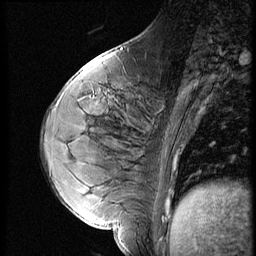
Breast MRI (dynamic contrast-enhanced), one sagittal slice. Slice 21 of 56 in the series (ordered by position). 3 images stored at this slice position (order not interpretable as contrast timing). 1.5 T. TE 4.2 ms, TR 9 ms. 2.5 mm slice thickness. 256 × 256 image matrix, field of view 180 × 180 mm. Patient: female, 35 years. From the clinical record (not read from this slice): setting: breast cancer imaged before/during neoadjuvant chemotherapy; receptor status: HR-positive, HER2-negative.
Outlined on this slice (semi-automatically segmented with operator editing):
- analysis volume of interest (the breast-tissue region the enhancement analysis was run in; not a lesion): bounding box [x1, y1, x2, y2] px = [58, 70, 171, 208]
- tumour enhancement mask (voxels above the 140 % enhancement threshold inside the analysis volume of interest): [166, 202, 169, 208]